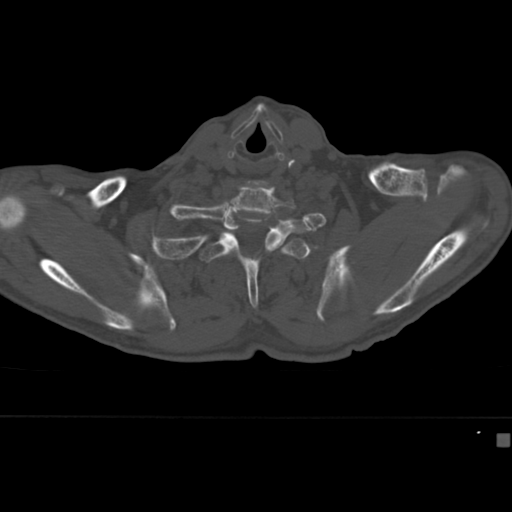
CT including the spine, one axial slice; position 349 of 430 along the scan axis; 120 kVp; bone window (W 1800 / L 400 HU); 512 × 512 image matrix, field of view 337 × 337 mm. Patient: male, 64 years. Case-level facts recorded for this patient, not image findings: primary cancer: uterus; vertebrae with lytic lesions (as recorded): T1, T4, T5, T7, L5.
Annotated regions visible in this slice (semi-automatically segmented with operator editing):
- T2 vertebra: box from (x=200, y=235) to (x=311, y=308) px